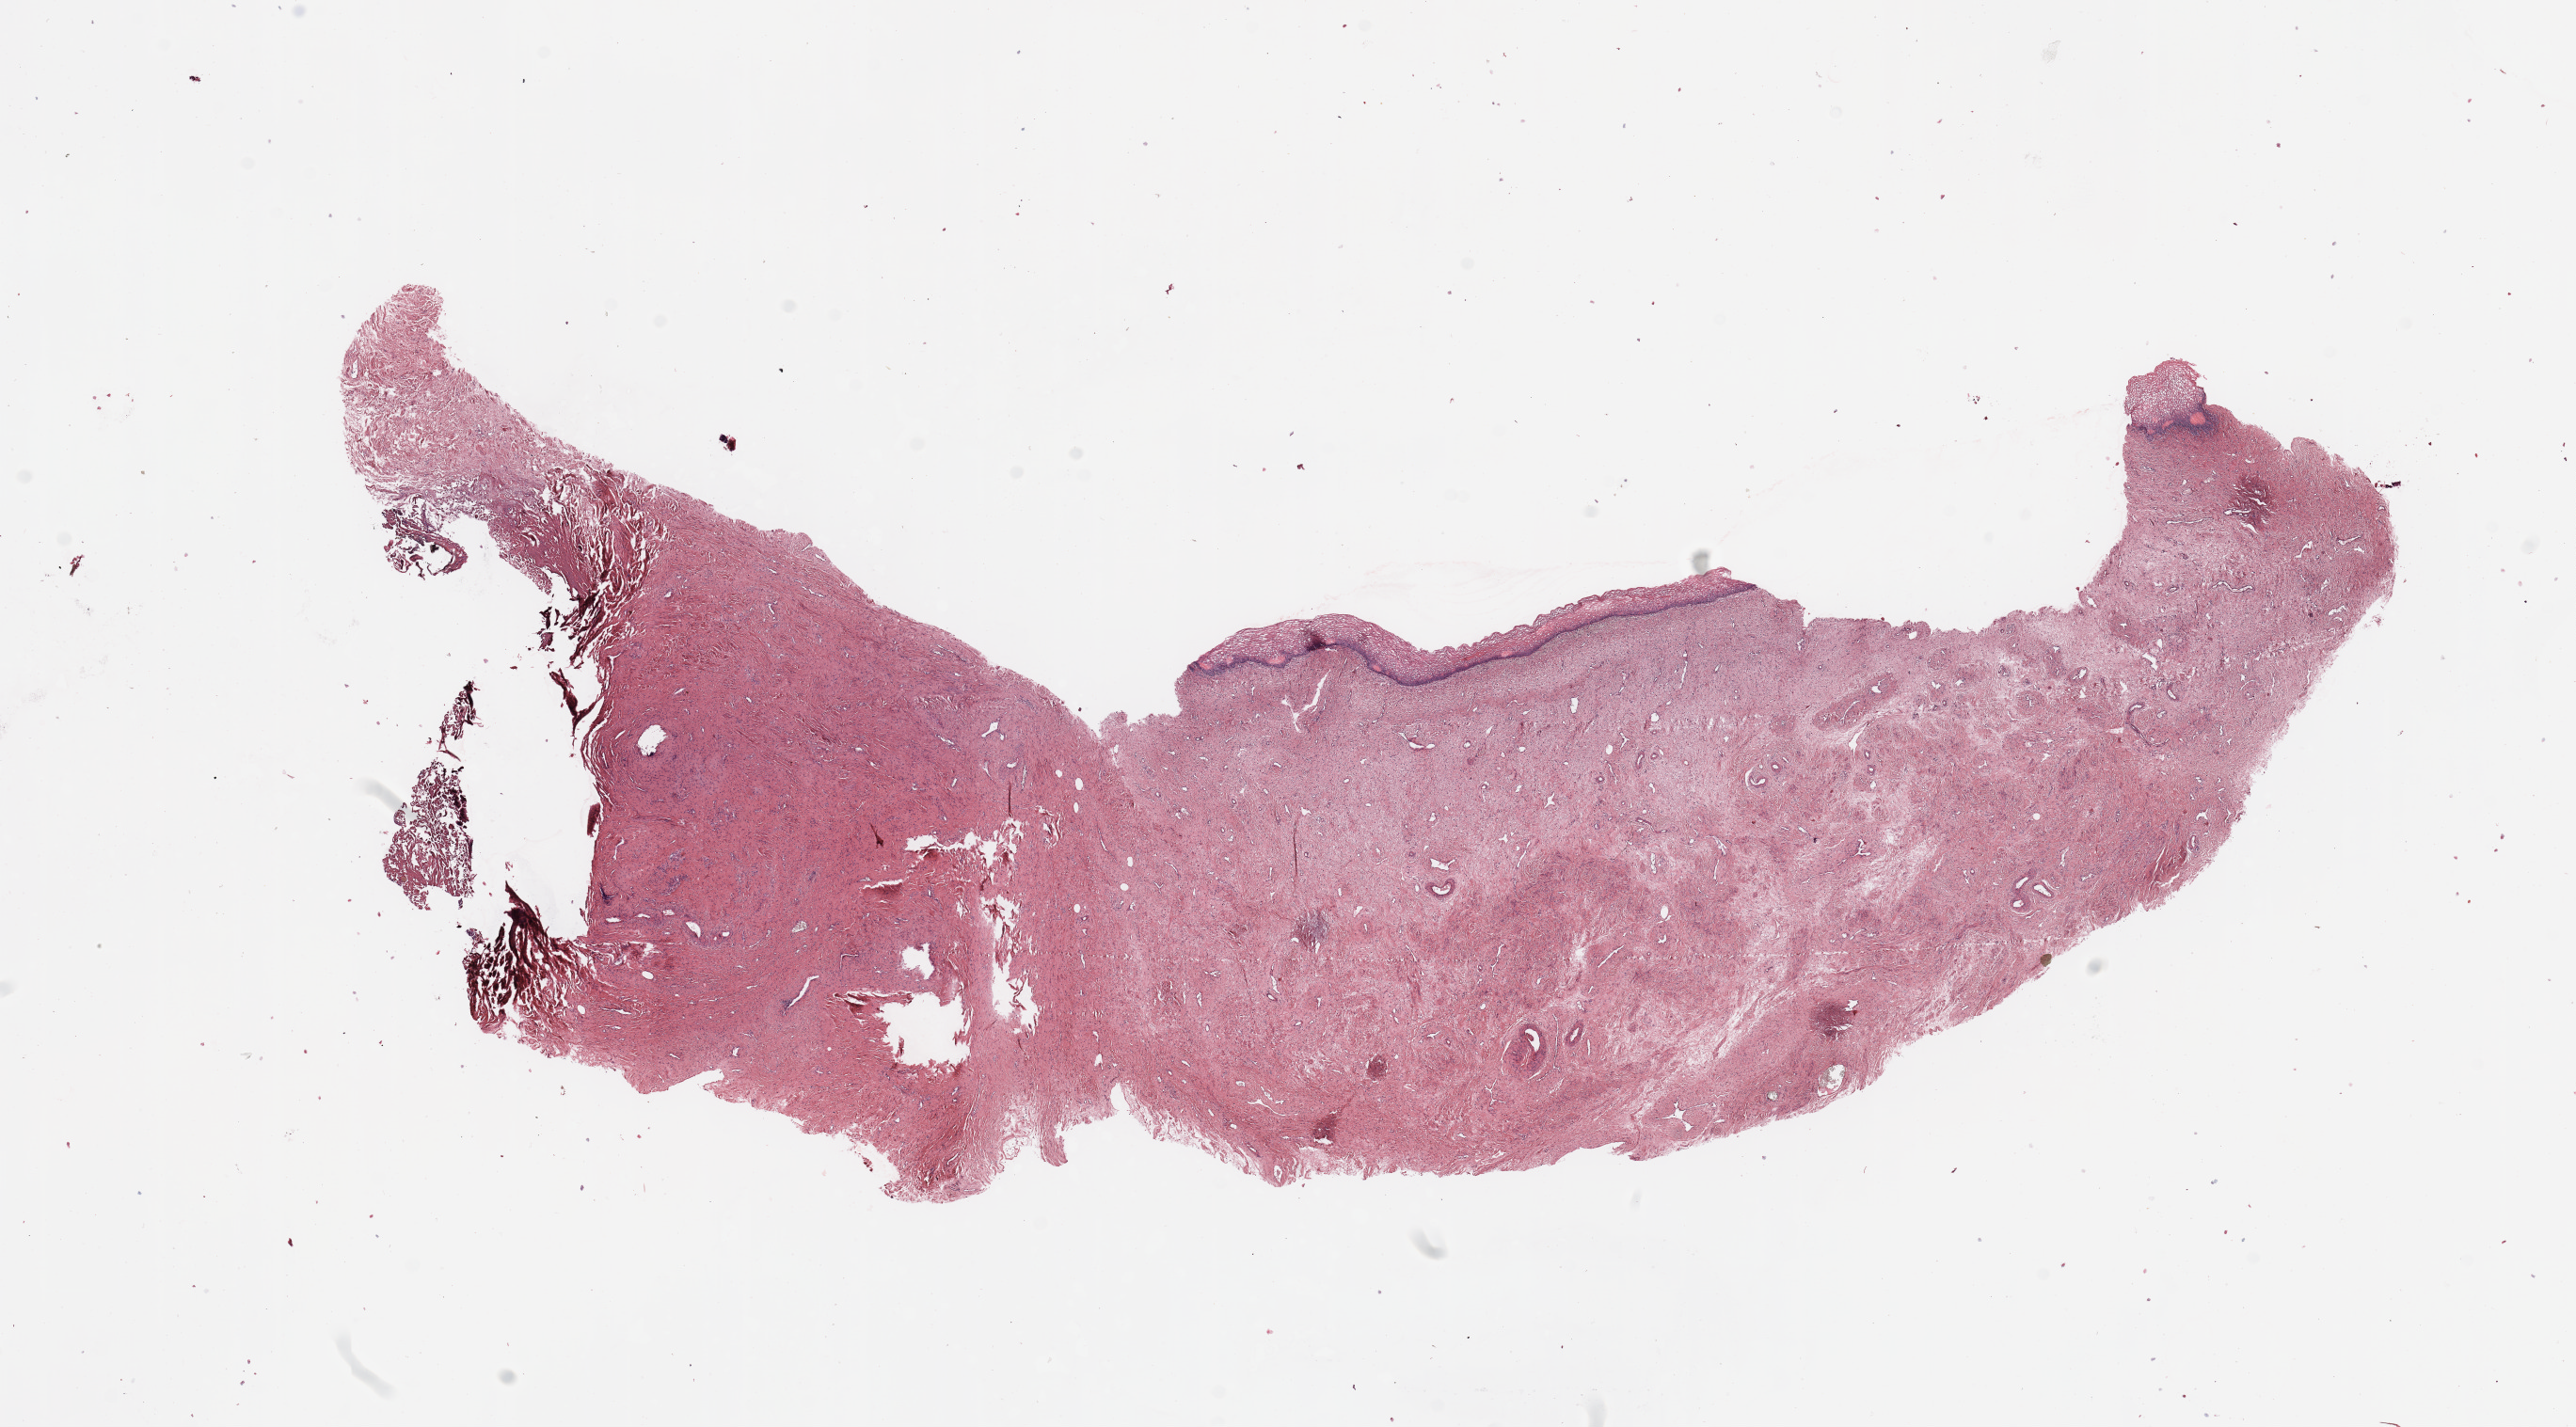
Whole-slide histology image, H&E-stained, shown as a low-resolution overview of the whole scanned area (about 21.7 x 12.0 mm, acquisition: 20x scan); normal (non-tumour) tissue sample, sampled site: uterus. Patient: female, age 66 years.
This section: normal (non-tumour) tissue from the same patient. Patient diagnosis: Endometrioid adenocarcinoma, NOS.